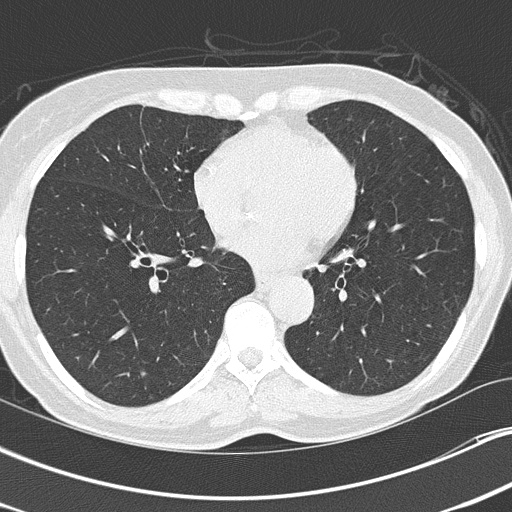
Axial slice from a low-dose chest CT screening exam; second screening round (one year after baseline); lung window (W 1500 / L -600 HU); lung (sharp) reconstruction kernel (B50f). Female participant, aged 67 years at enrolment. Current smoker at enrolment.
Lesion marked by an expert reader, box from (x=126, y=365) to (x=159, y=392) px. The screening reader recorded 2 non-calcified nodules or masses ≥4 mm on this exam (right lower lobe, left lower lobe); which of them this box marks is not recorded. Lung cancer was diagnosed 507 days after this screen: adenocarcinoma, NOS, left lower lobe, poorly differentiated (G3), stage IA (AJCC 6th edition), 25 mm at pathology.